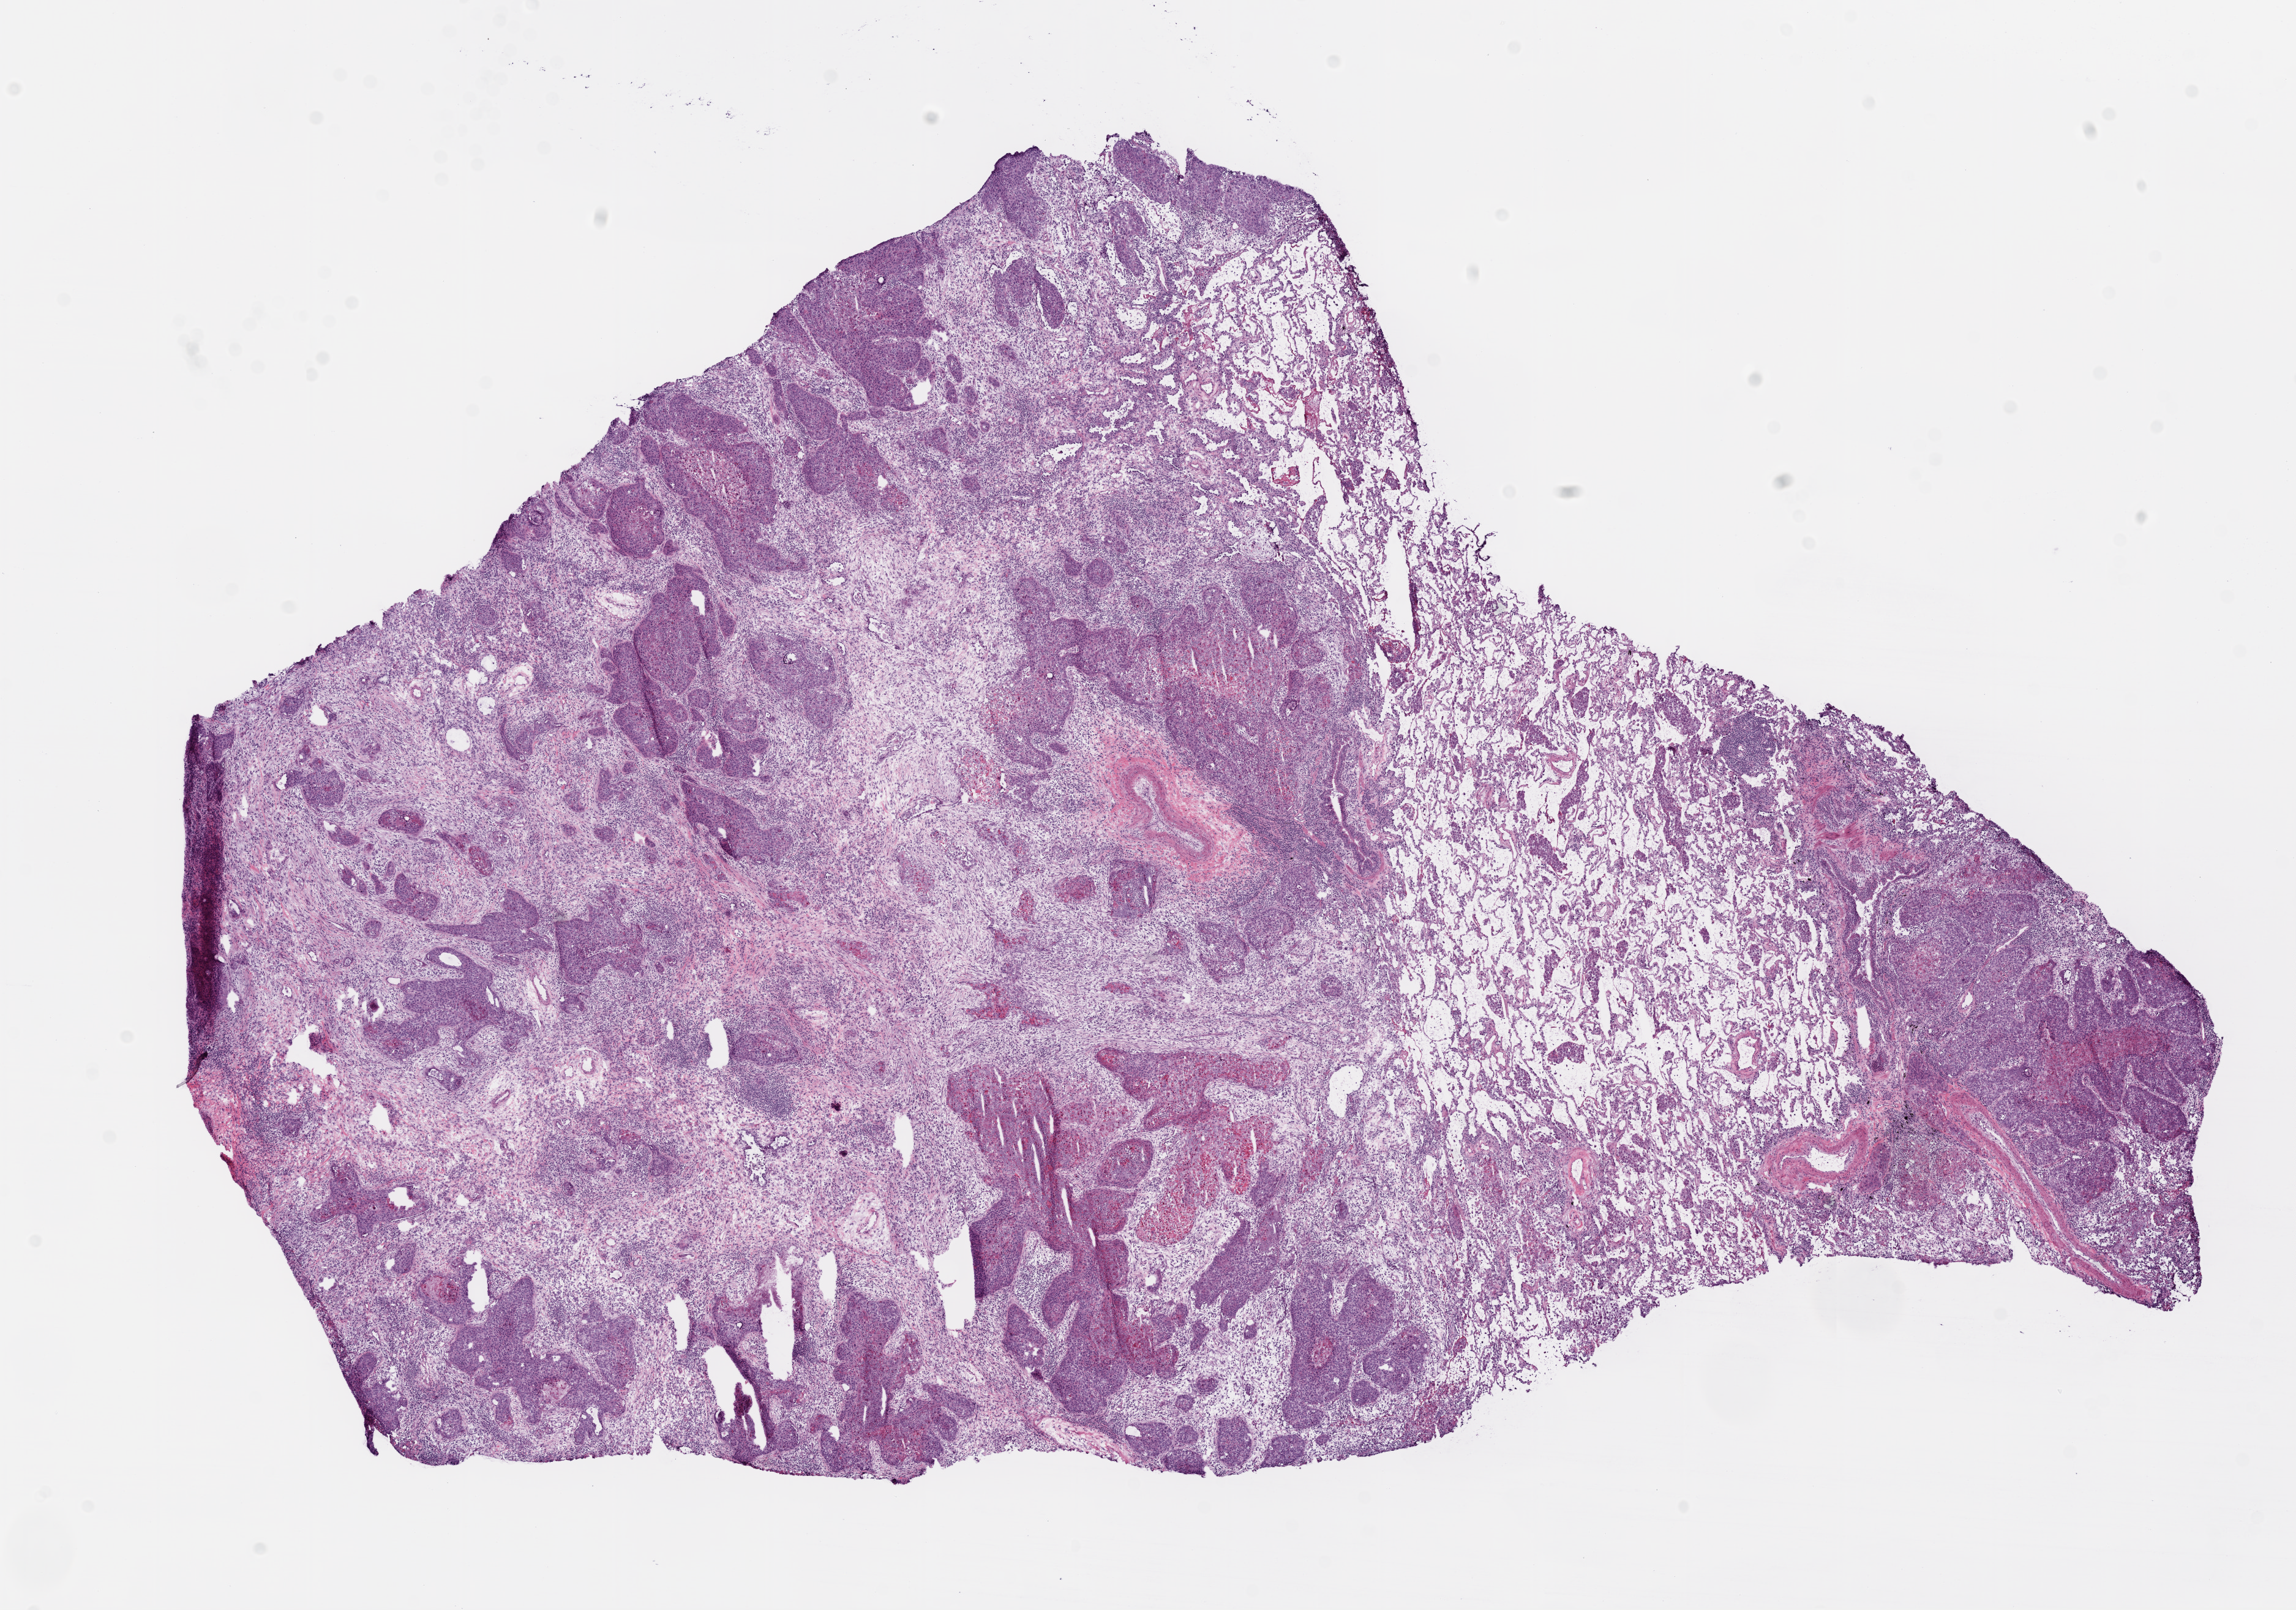
Digitized H&E tissue section (whole slide), whole scanned area (about 15.0 x 10.6 mm) shown as a low-resolution overview; frozen section from the bottom of the tissue portion; lung, primary tumour sample. Male patient; age at initial diagnosis 74 years. Slide review estimates, as recorded: tumour cells 60%, tumour nuclei 60%, normal cells 15%, stromal cells 20%, necrosis 5%.
AJCC pathologic stage: IB. Pathologic diagnosis: Squamous cell carcinoma, NOS (upper lobe, lung). Laterality: left.